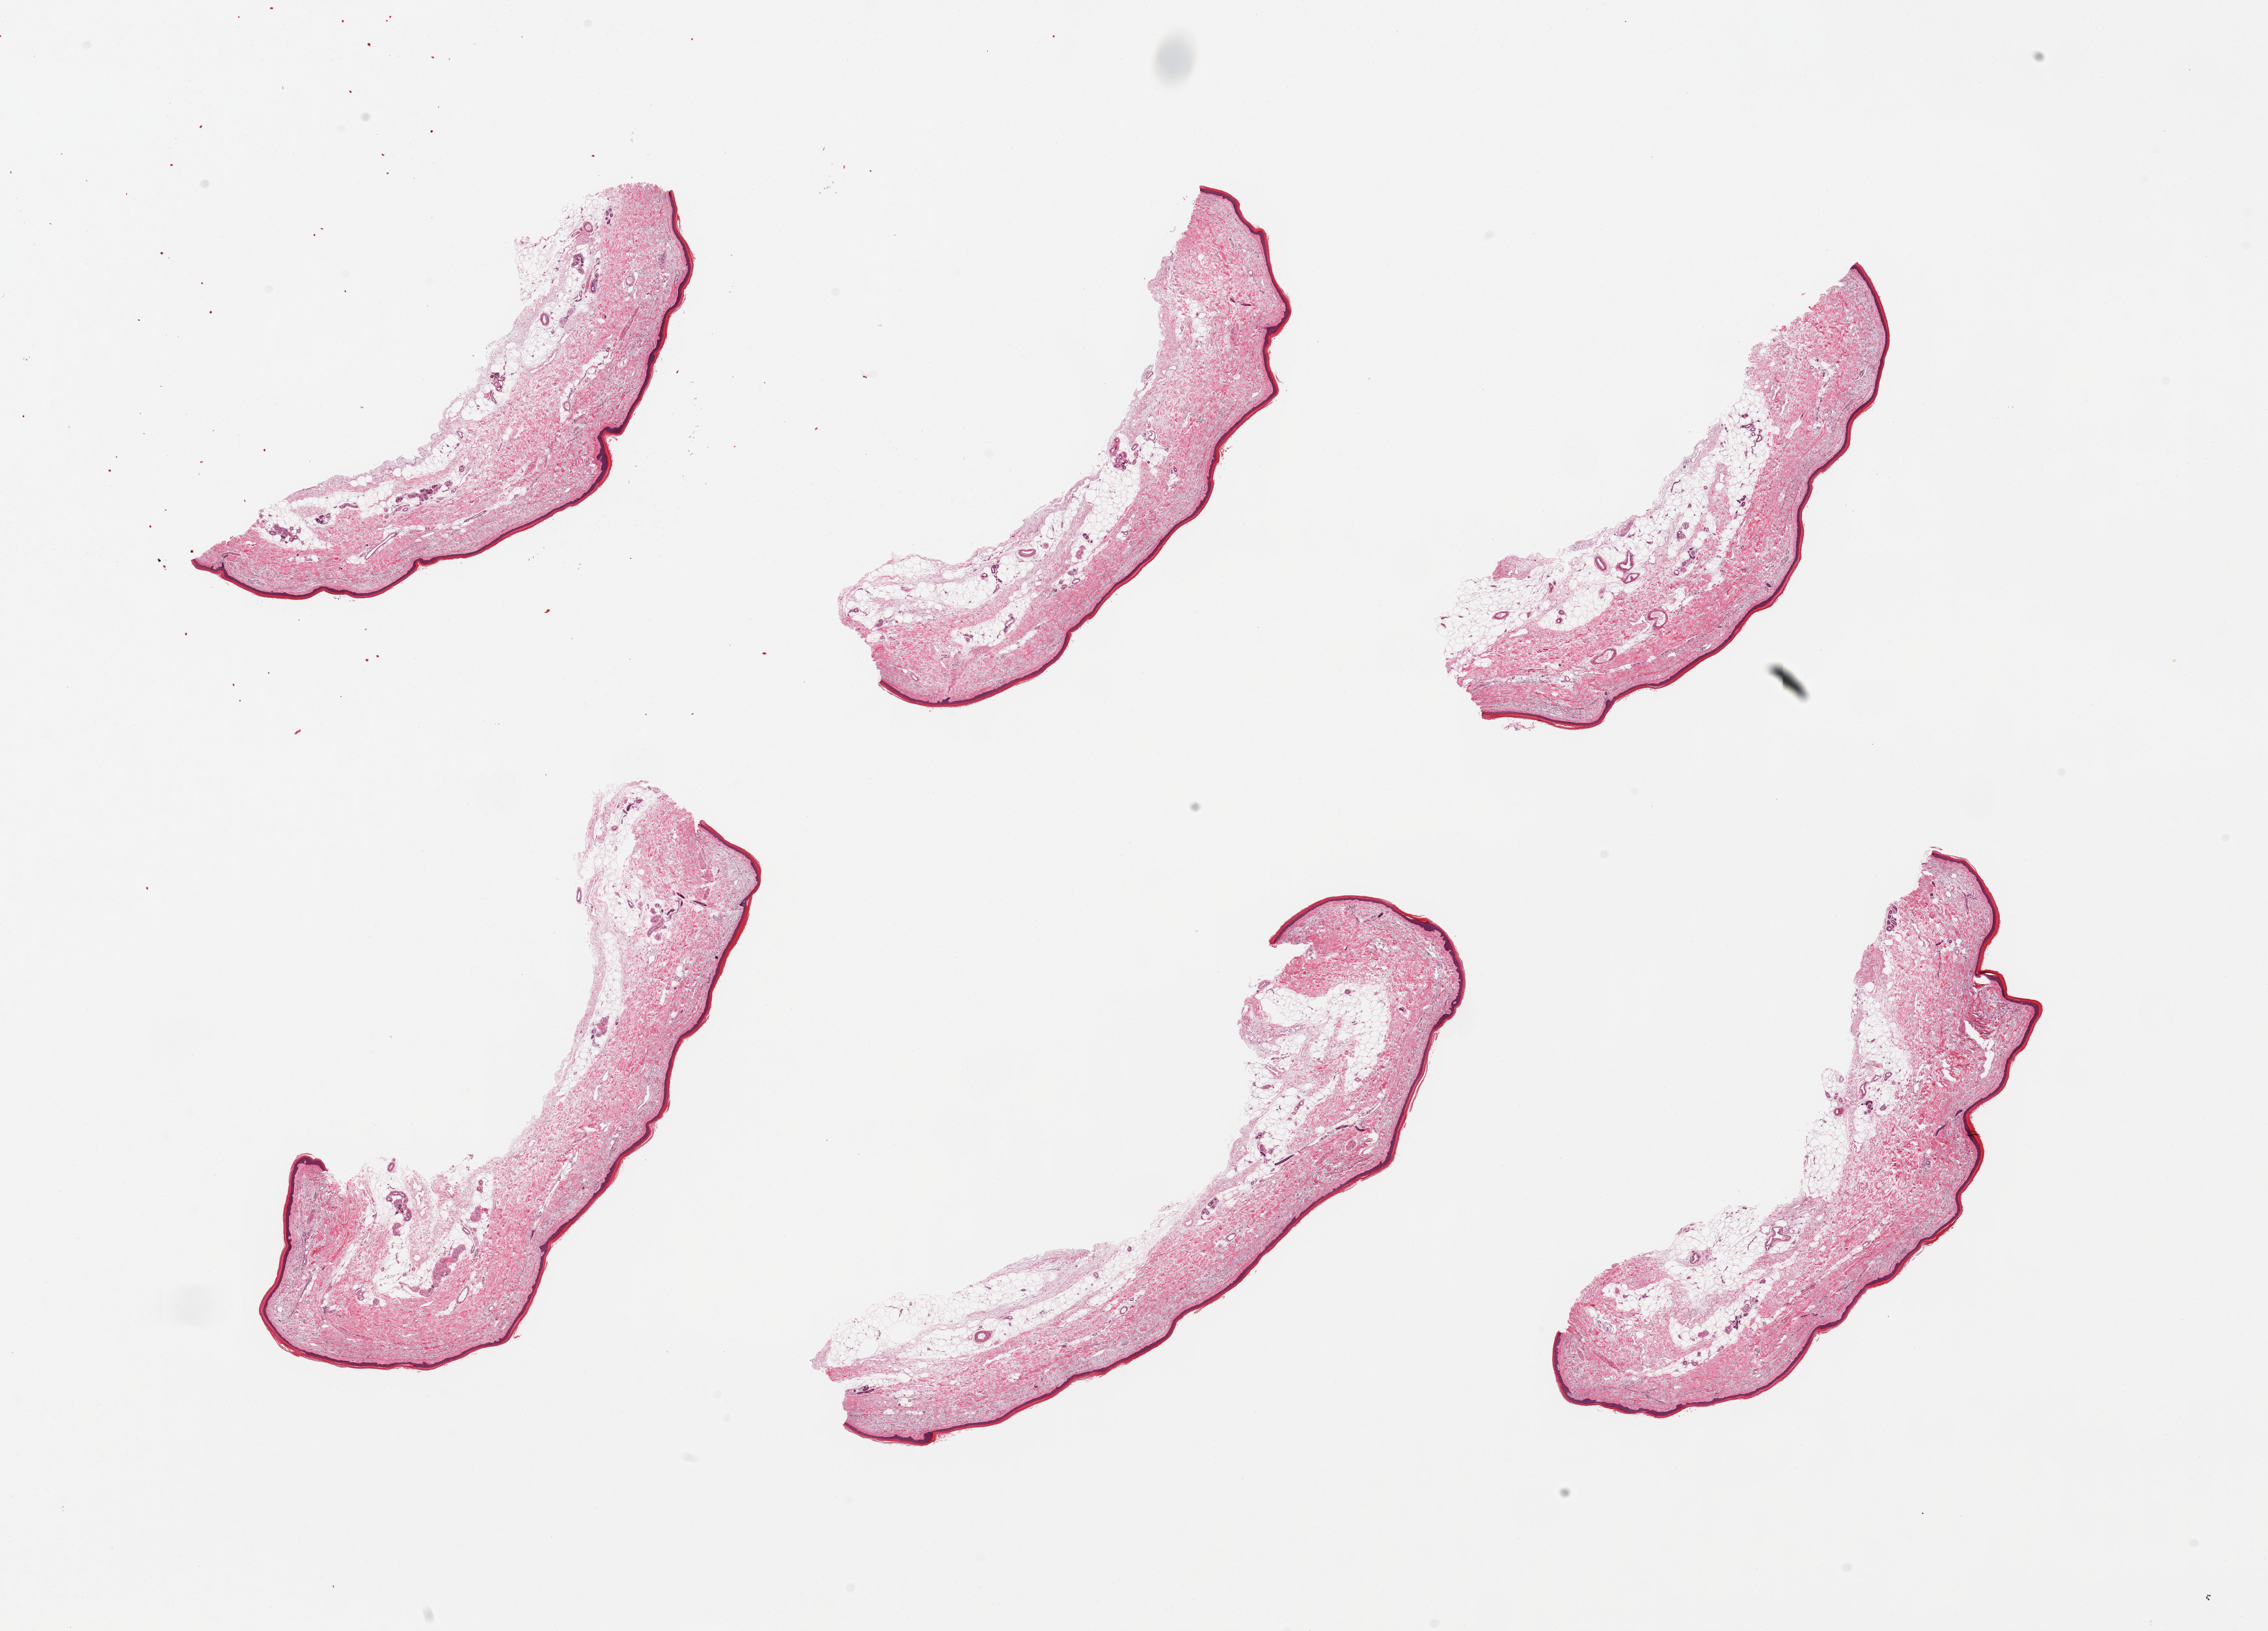
Haematoxylin and eosin whole-slide image, brightfield, whole scanned area (about 27.6 x 19.8 mm, slide scanned at 20x) shown as a low-resolution overview, PAXgene-fixed, paraffin-embedded tissue, section of skin of lower leg (target tissue), tissue donor sample. Male donor.
Reviewer comment on this tissue sample: 6 pieces; hyperkeratosis; dermal mucinous change; 20% intradermal fat.